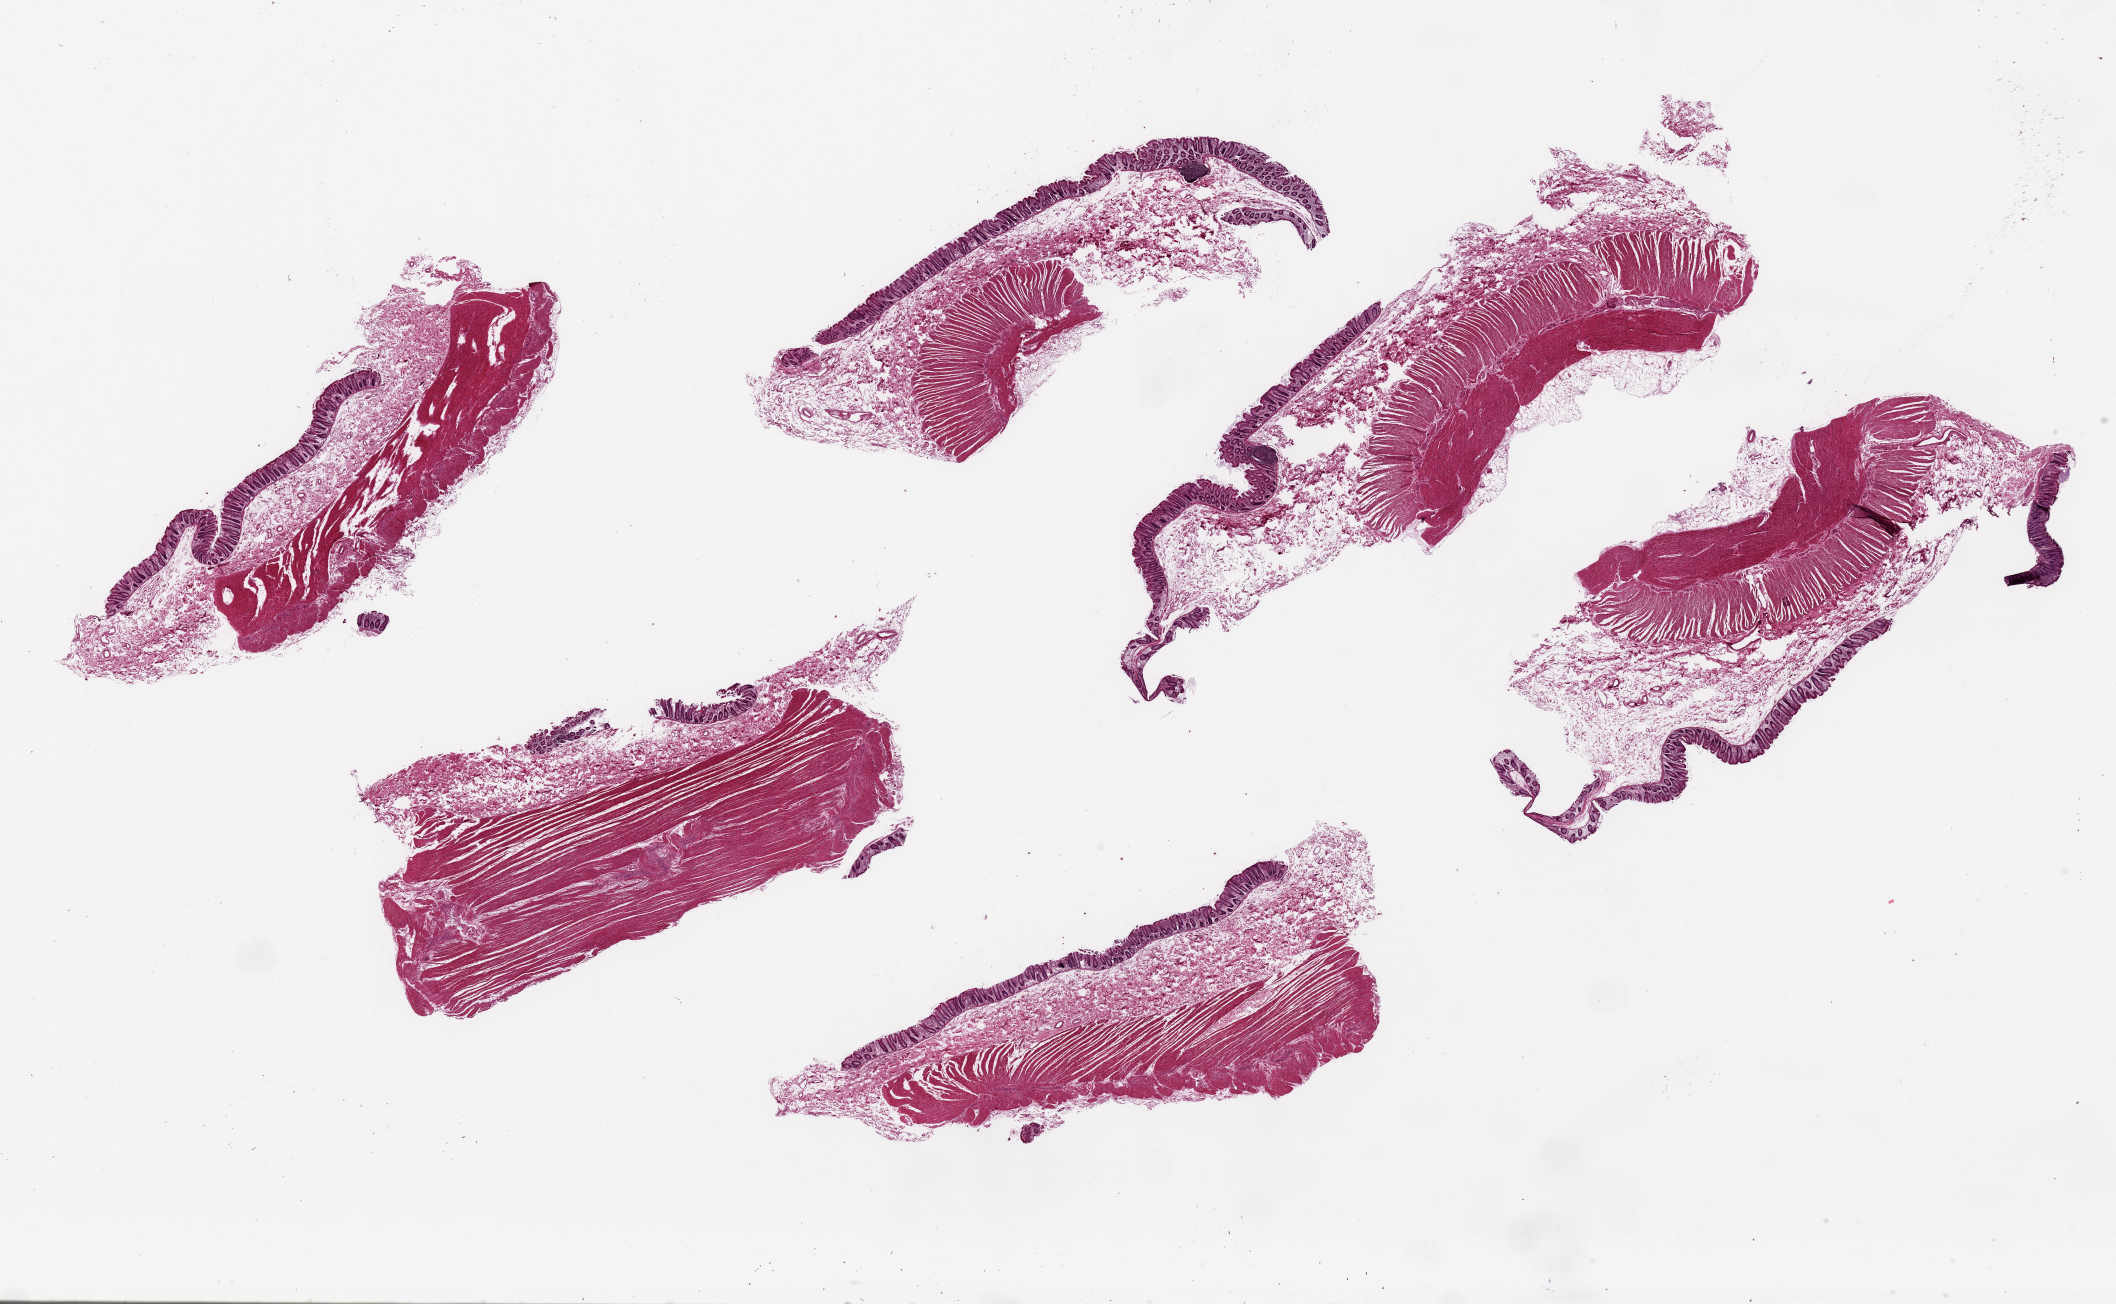
Whole-slide image, H&E stain, shown as a low-resolution overview of the whole scanned area (about 33.5 x 20.6 mm, from a 20x scan). PAXgene-fixed paraffin-embedded (PFPE) section. Section of transverse colon (target tissue). Tissue donor sample. Male donor.
Review note (as recorded): 6 ~8.5x3mm pieces; mucosa is generally well-preserved, ~ 10% of thickness.